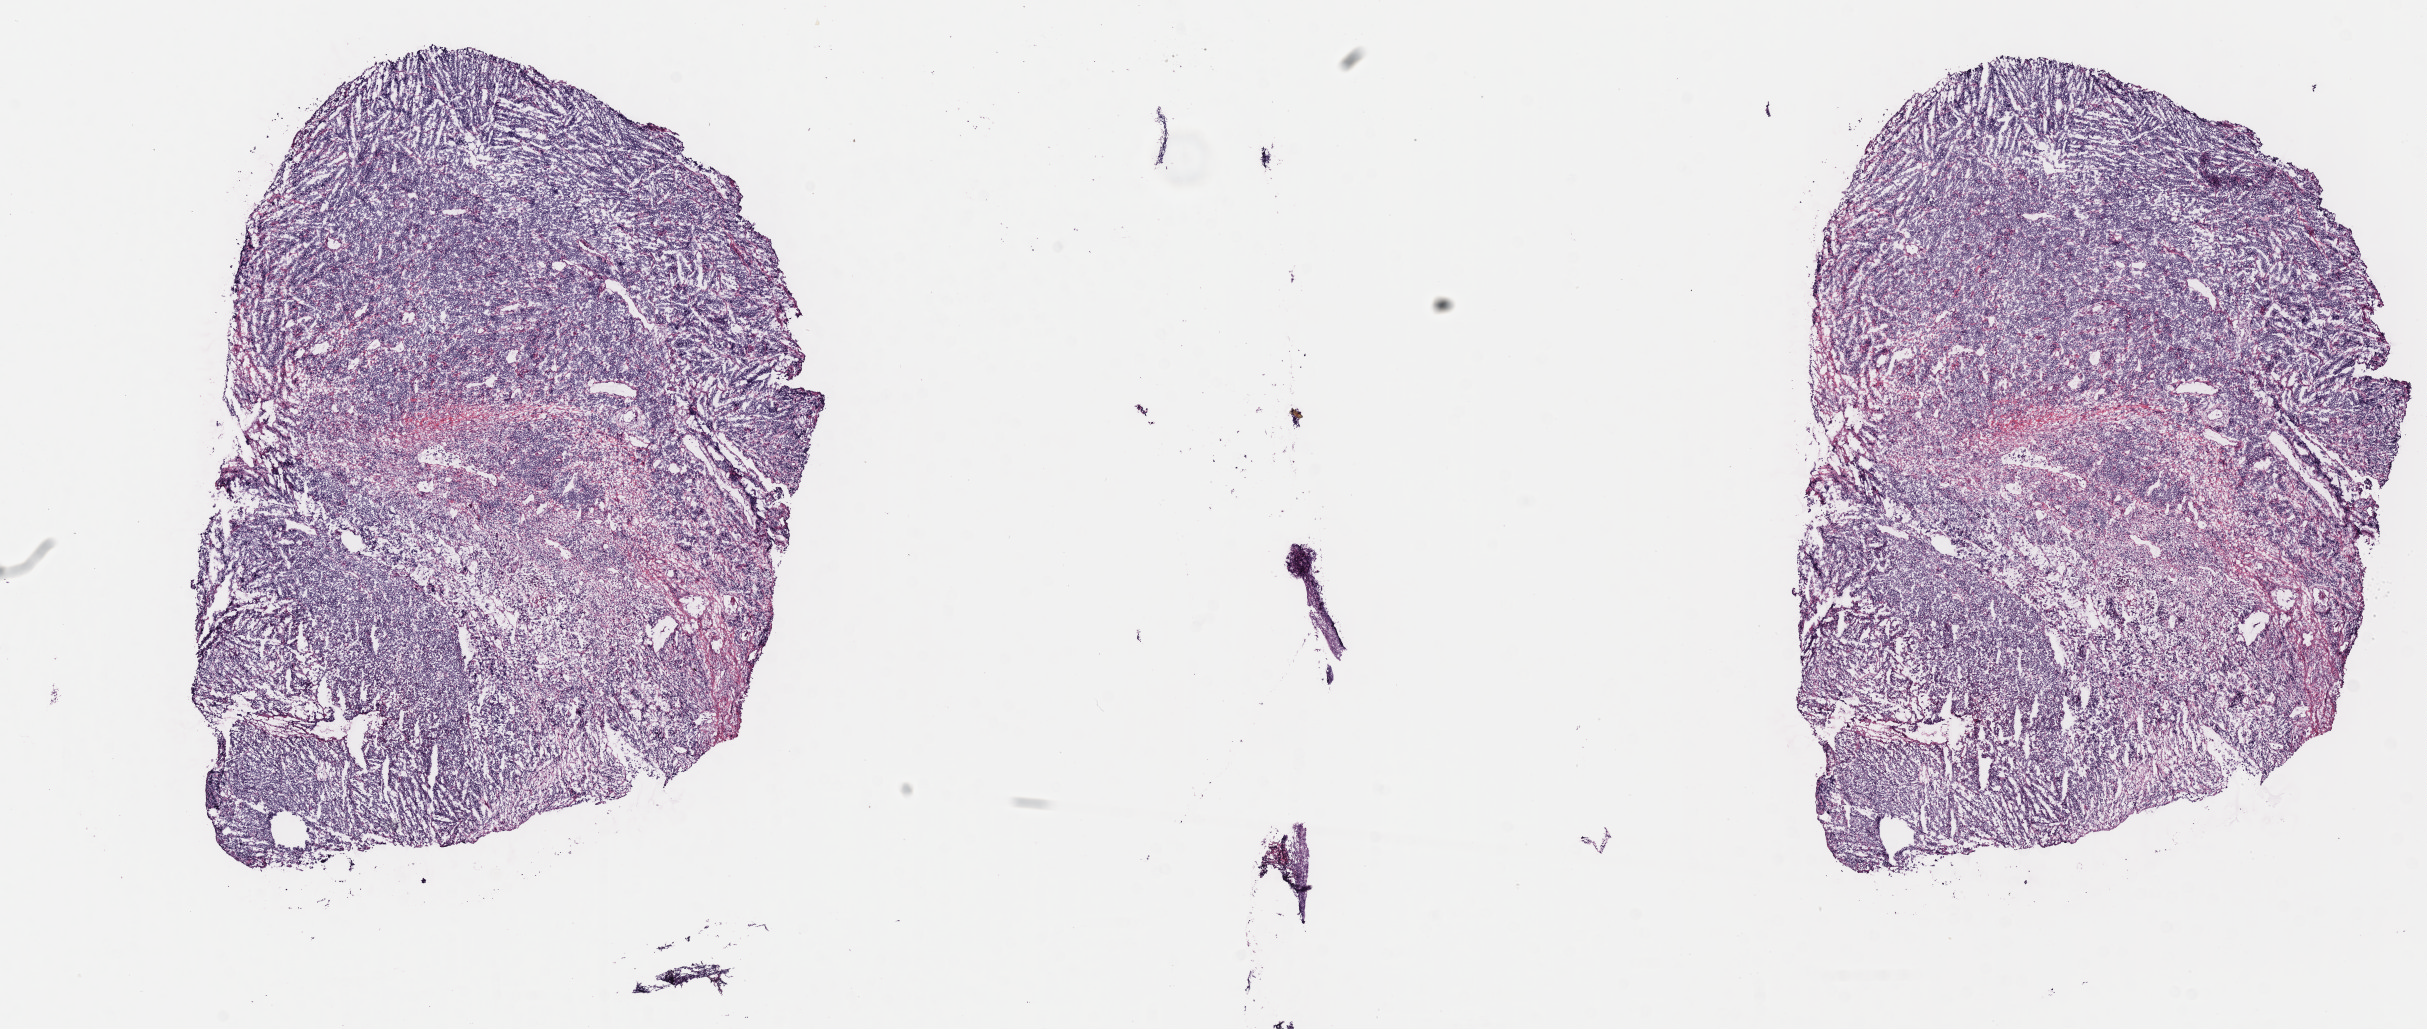
Hematoxylin and eosin (H&E) whole-slide image — low-resolution overview of the scanned area, about 19.6 x 8.3 mm; frozen section; specimen: primary tumor; anatomic site: cranium. Male patient; age at initial diagnosis 7 years. Composition of this section per pathologist review: tumor cells 70%, tumor nuclei 90%, stromal cells 25%, necrosis 5%, normal cells 0%. Inflammatory infiltration, as recorded: lymphocyte infiltration 10%, monocyte infiltration 10%, neutrophil infiltration 0%.
* Ann Arbor stage (patient): Stage III
* section: bottom of the tissue portion
* diagnosis: Burkitt lymphoma, NOS